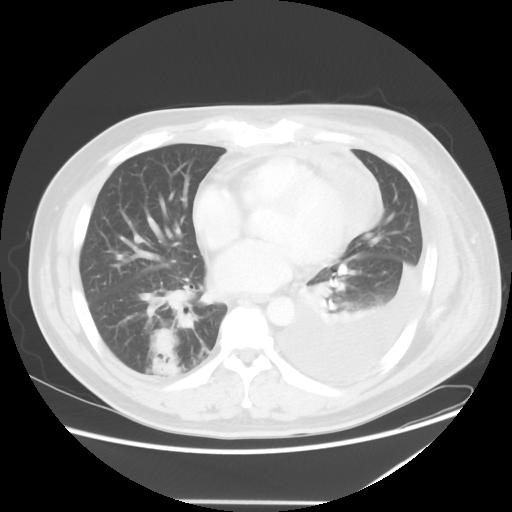
Chest CT, one axial slice; position 22 of 52 along the scan axis; reconstruction kernel STANDARD; lung window (W 1500 / L -600 HU); 512 × 512 image matrix, field of view 405 × 405 mm. Male patient, age 42 years. Case-level facts recorded for this patient, not image findings: clinical TNM (as recorded): T2 N1 M1.
Outlined on this slice (rectangle marked by the reading radiologist):
- lung tumour (recorded histology: adenocarcinoma): bounding box (x1, y1, x2, y2) in pixels: (142, 318, 184, 364)